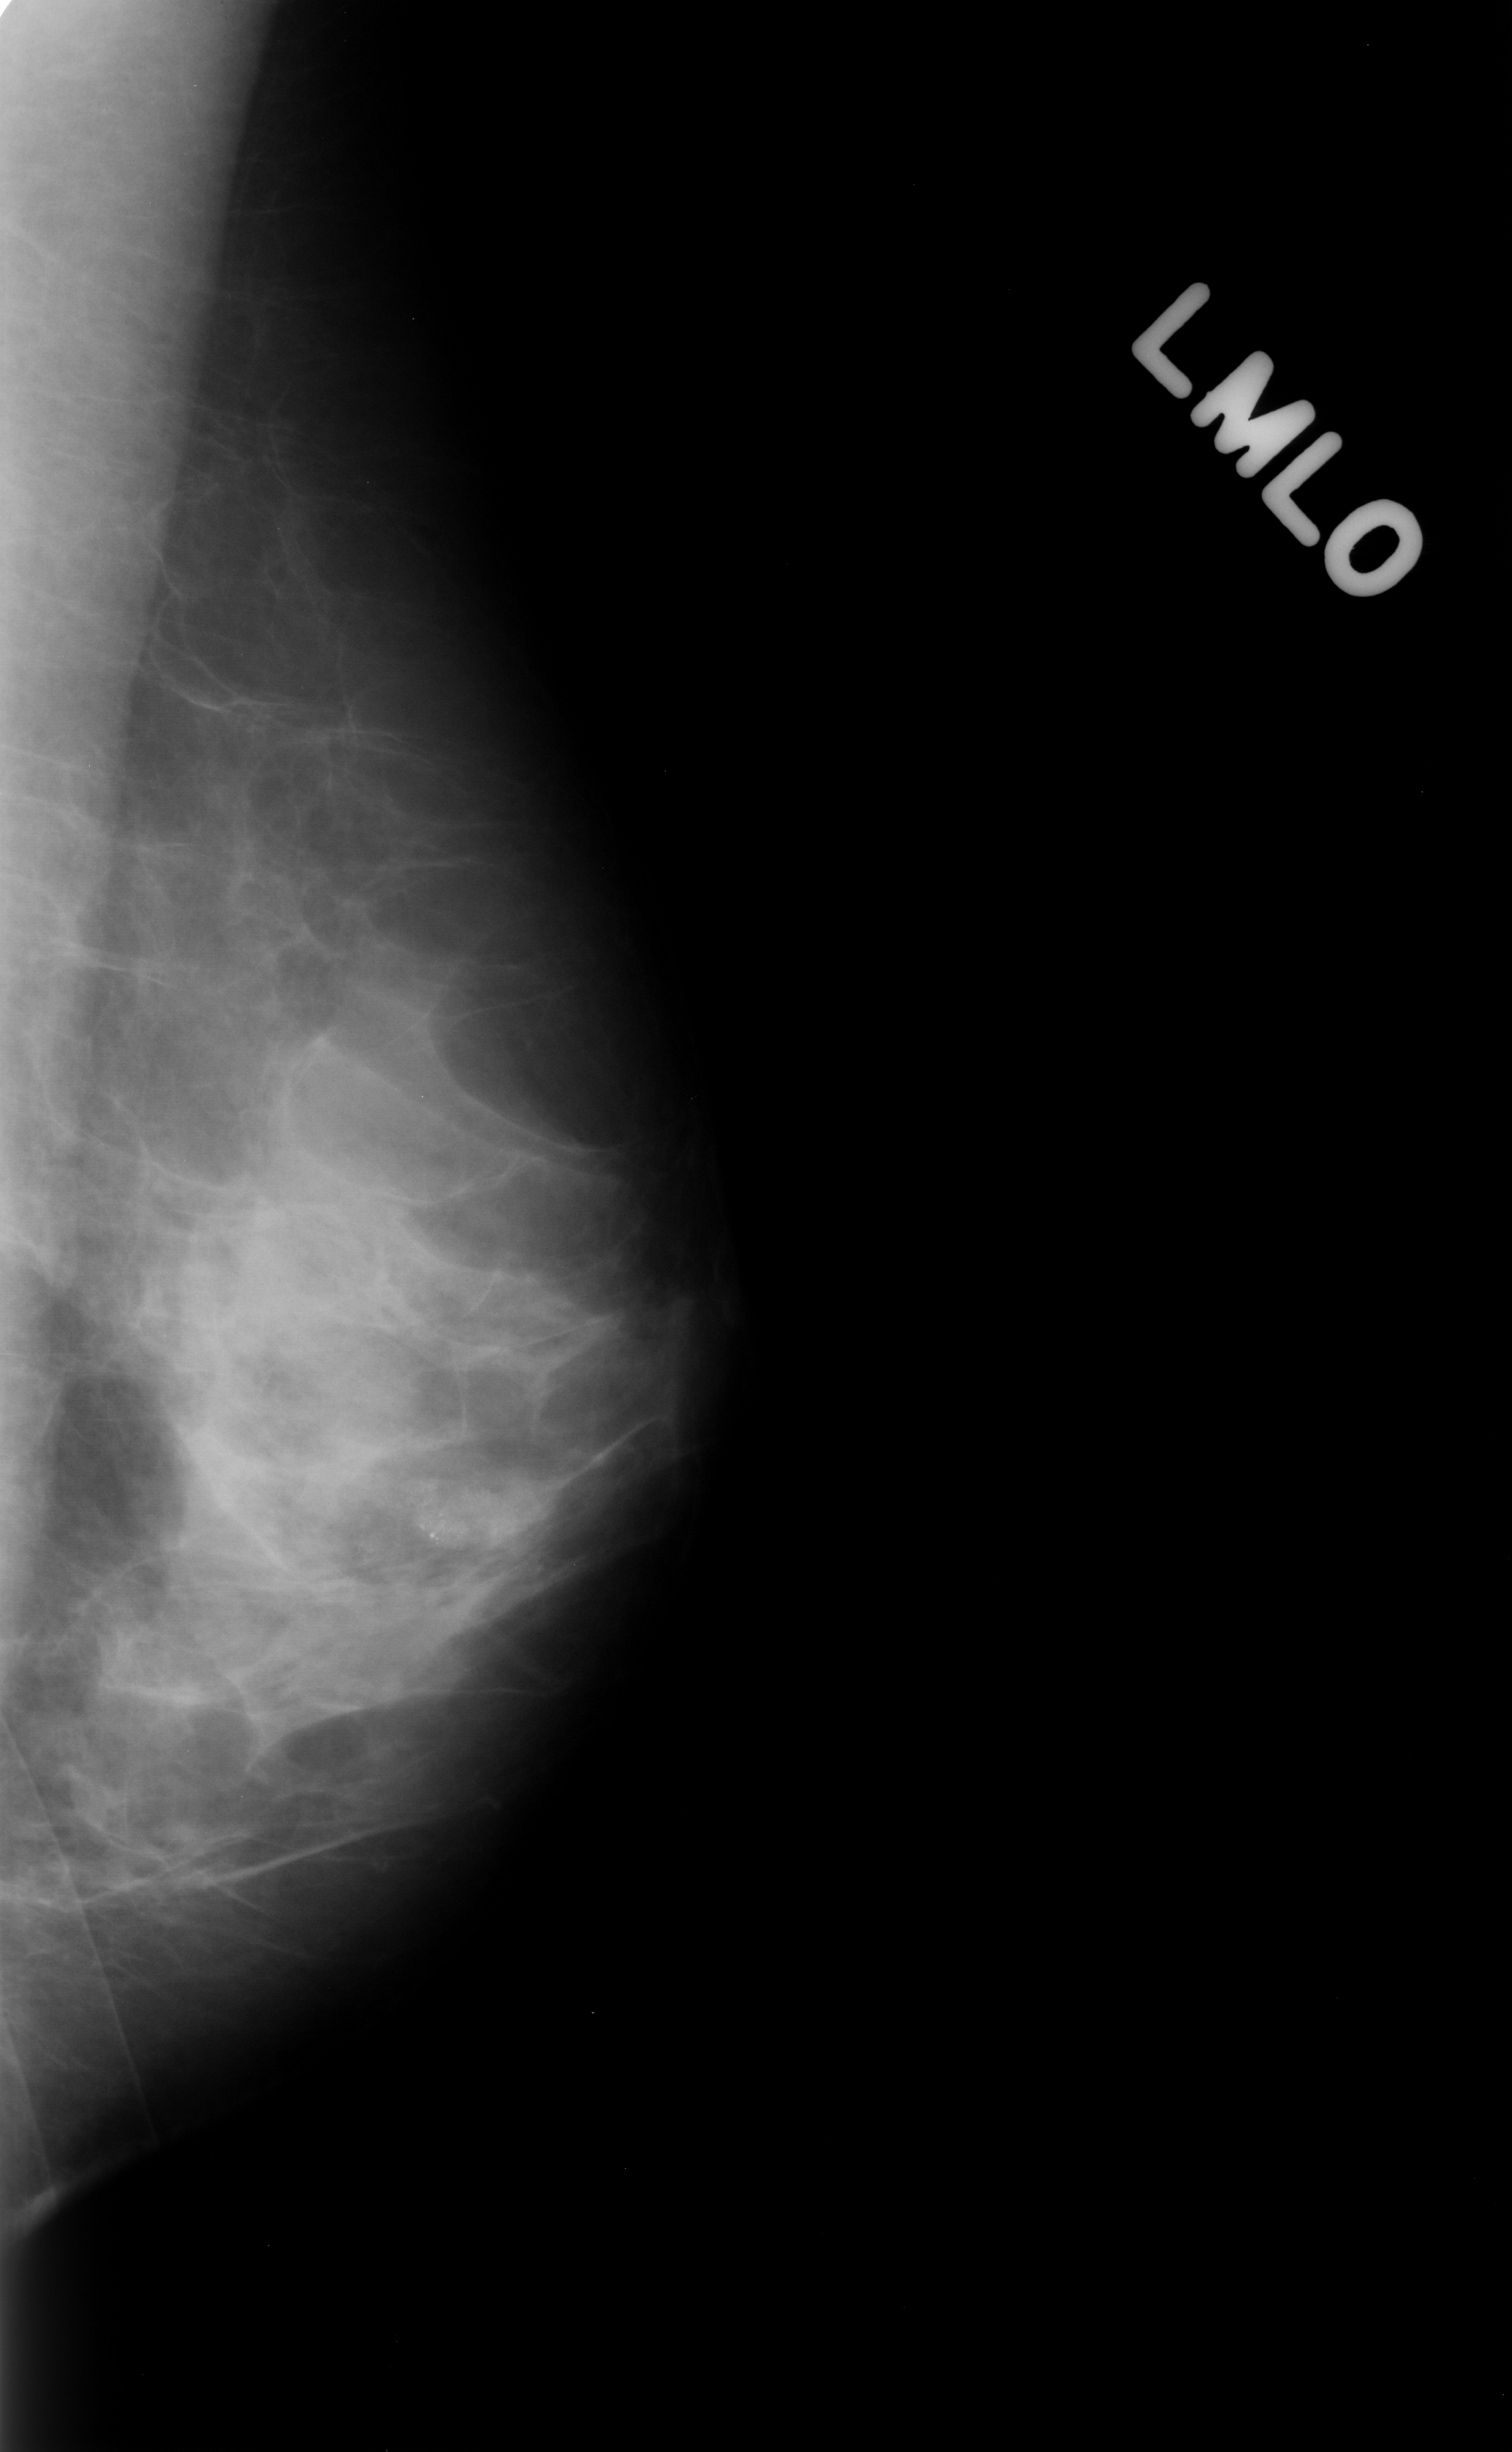
Digitized screen-film mammogram, left breast, MLO view, breast composition: heterogeneously dense (BI-RADS density category 3 of 4).
Calcifications, morphology pleomorphic, distribution clustered; BI-RADS assessment category 4; pathology (as recorded): benign.